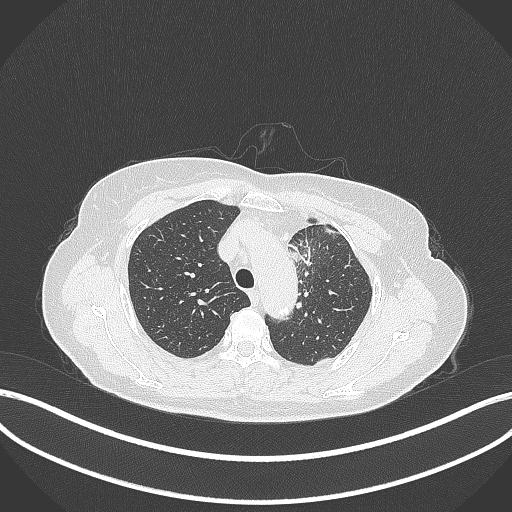
Chest CT, one axial slice; position 258 of 369 along the scan axis; reconstruction kernel B70f; lung window (W 1500 / L -600 HU); 1 mm slice thickness; 512 × 512 image matrix. Patient: female, 65 years. From the clinical record (not read from this slice): clinical TNM (as recorded): T2a N0 M0; histopathological grade: G2-3.
Outlined on this slice (rectangle marked by the reading radiologist):
- lung tumour (recorded histology: adenocarcinoma): box from (x=284, y=232) to (x=312, y=271) px